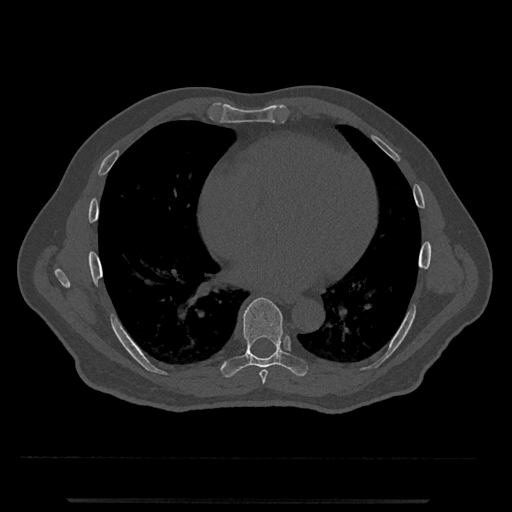
CT including the spine, one axial slice; slice 637 of 797 in the series (ordered by position); reconstruction kernel Br40s/3; 120 kVp; bone window (W 1800 / L 400 HU); 0.5 mm slice thickness; 512 × 512 image matrix, field of view 419 × 419 mm. Male patient, age 63 years. From the clinical record (not read from this slice): primary cancer: prostate.
Outlined on this slice (semi-automatically segmented with operator editing):
- T7 vertebra: bounding box <259,369,268,385> (left, top, right, bottom; pixels)
- T8 vertebra: <220,297,308,378>